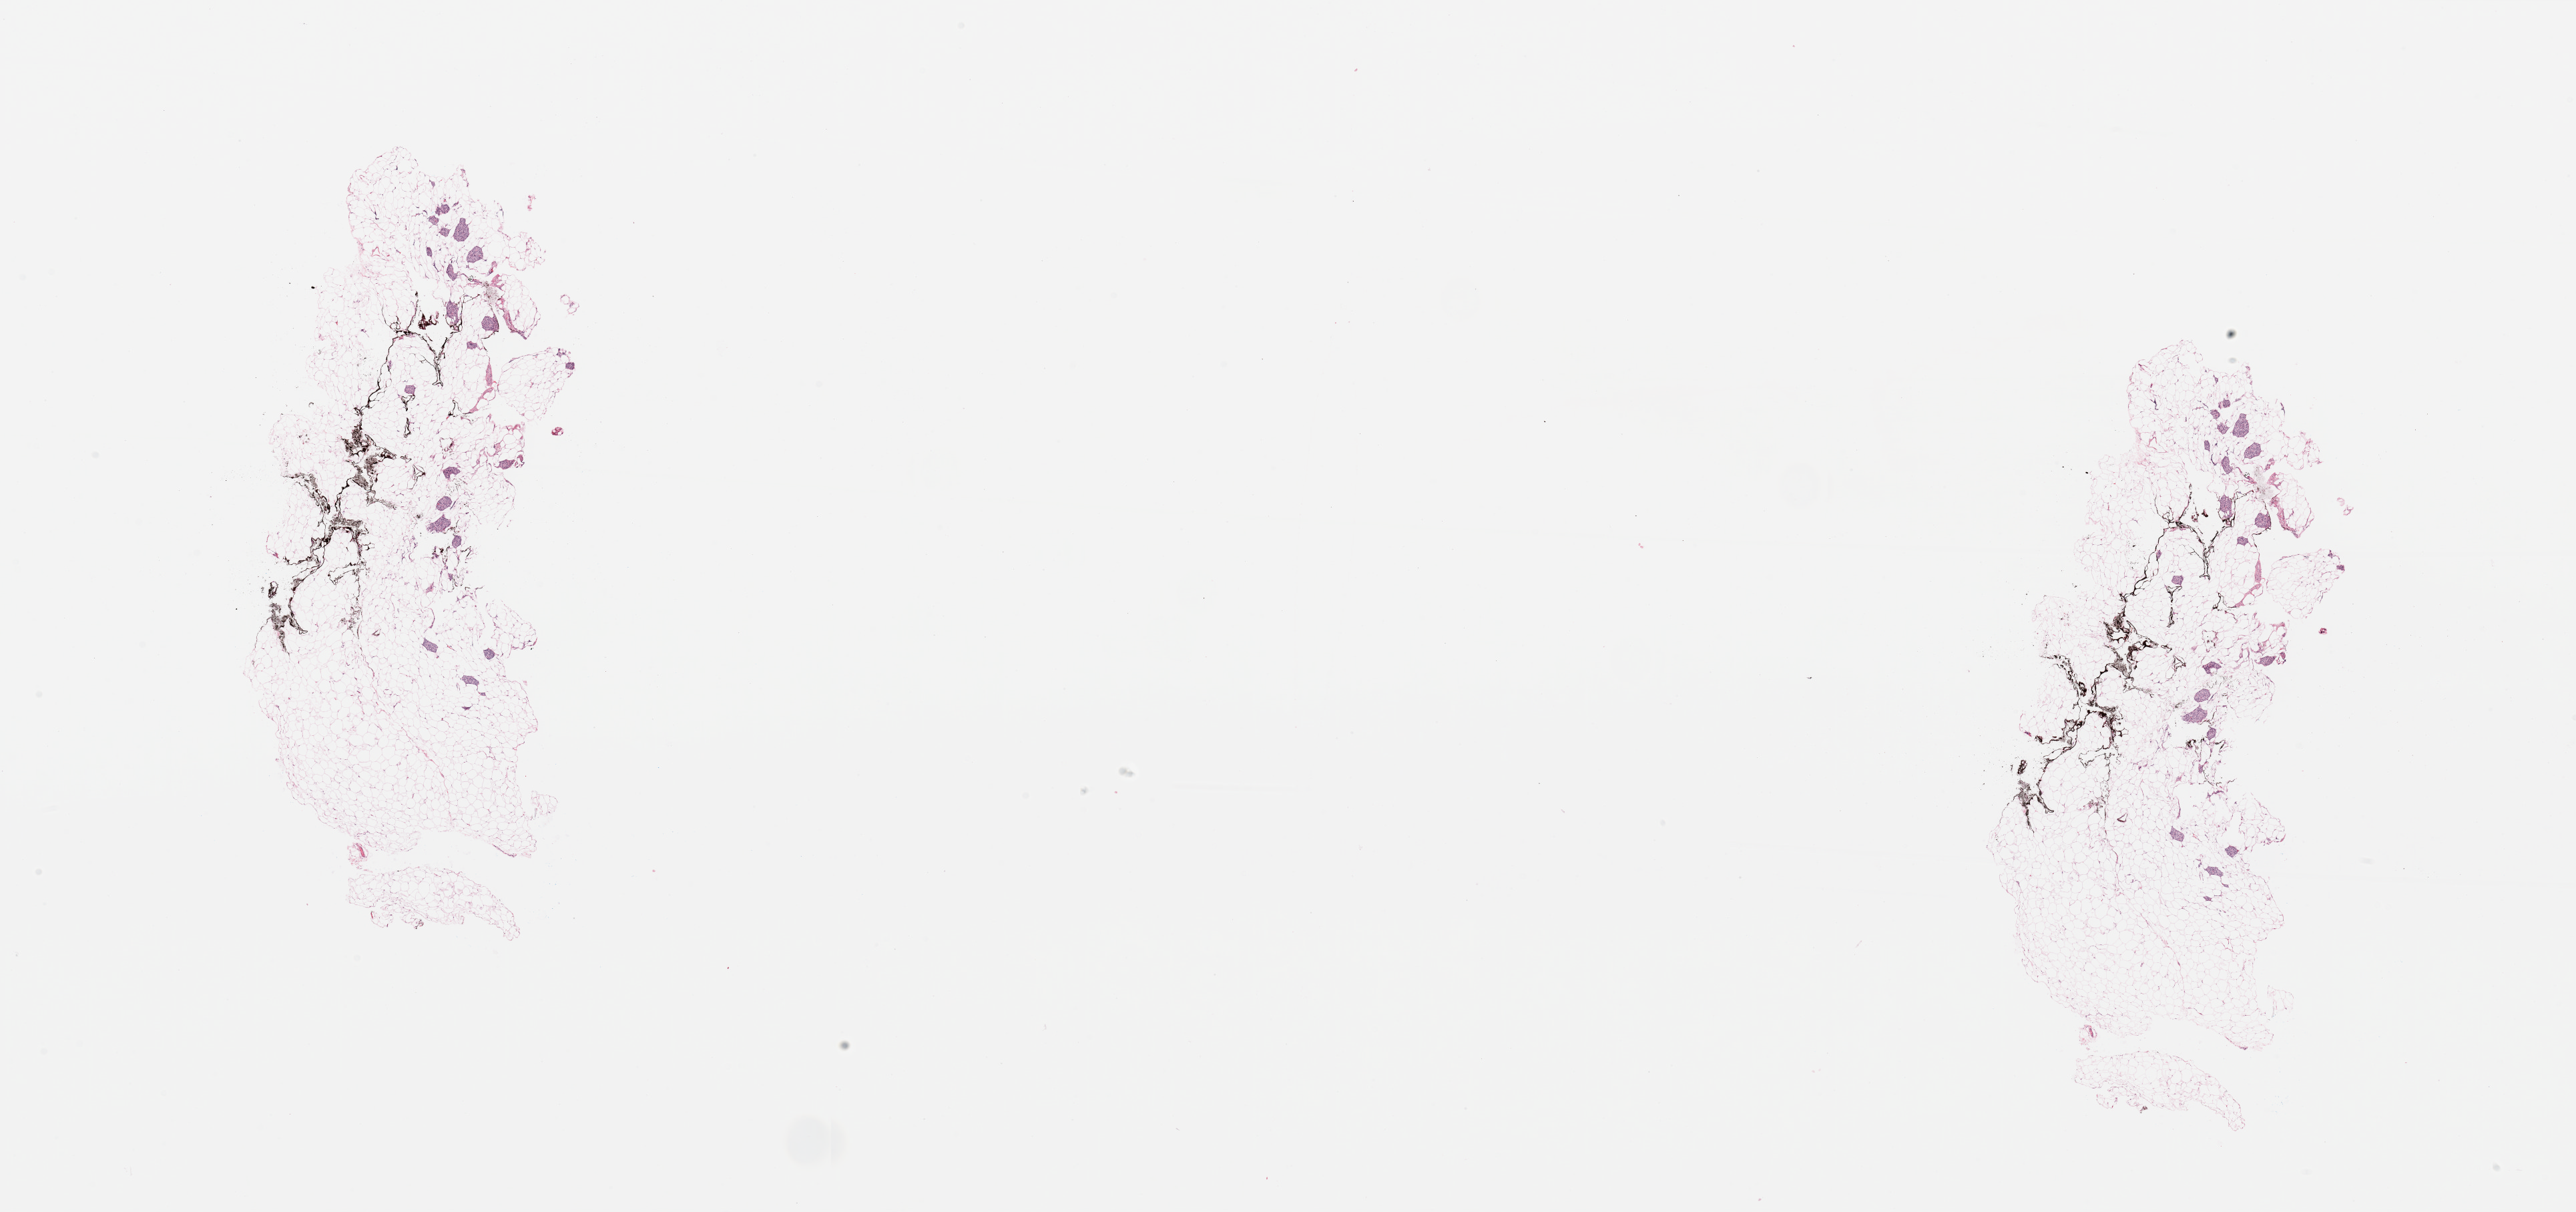
H&E whole-slide image — a low-resolution overview of the entire scanned area, about 30.5 x 14.4 mm (from a 20x scan). Normal (non-tumour) tissue sample, pancreas. Patient: female, age 79 years.
* this section: normal (non-tumour) tissue from the same patient
* patient diagnosis: Infiltrating duct carcinoma, NOS